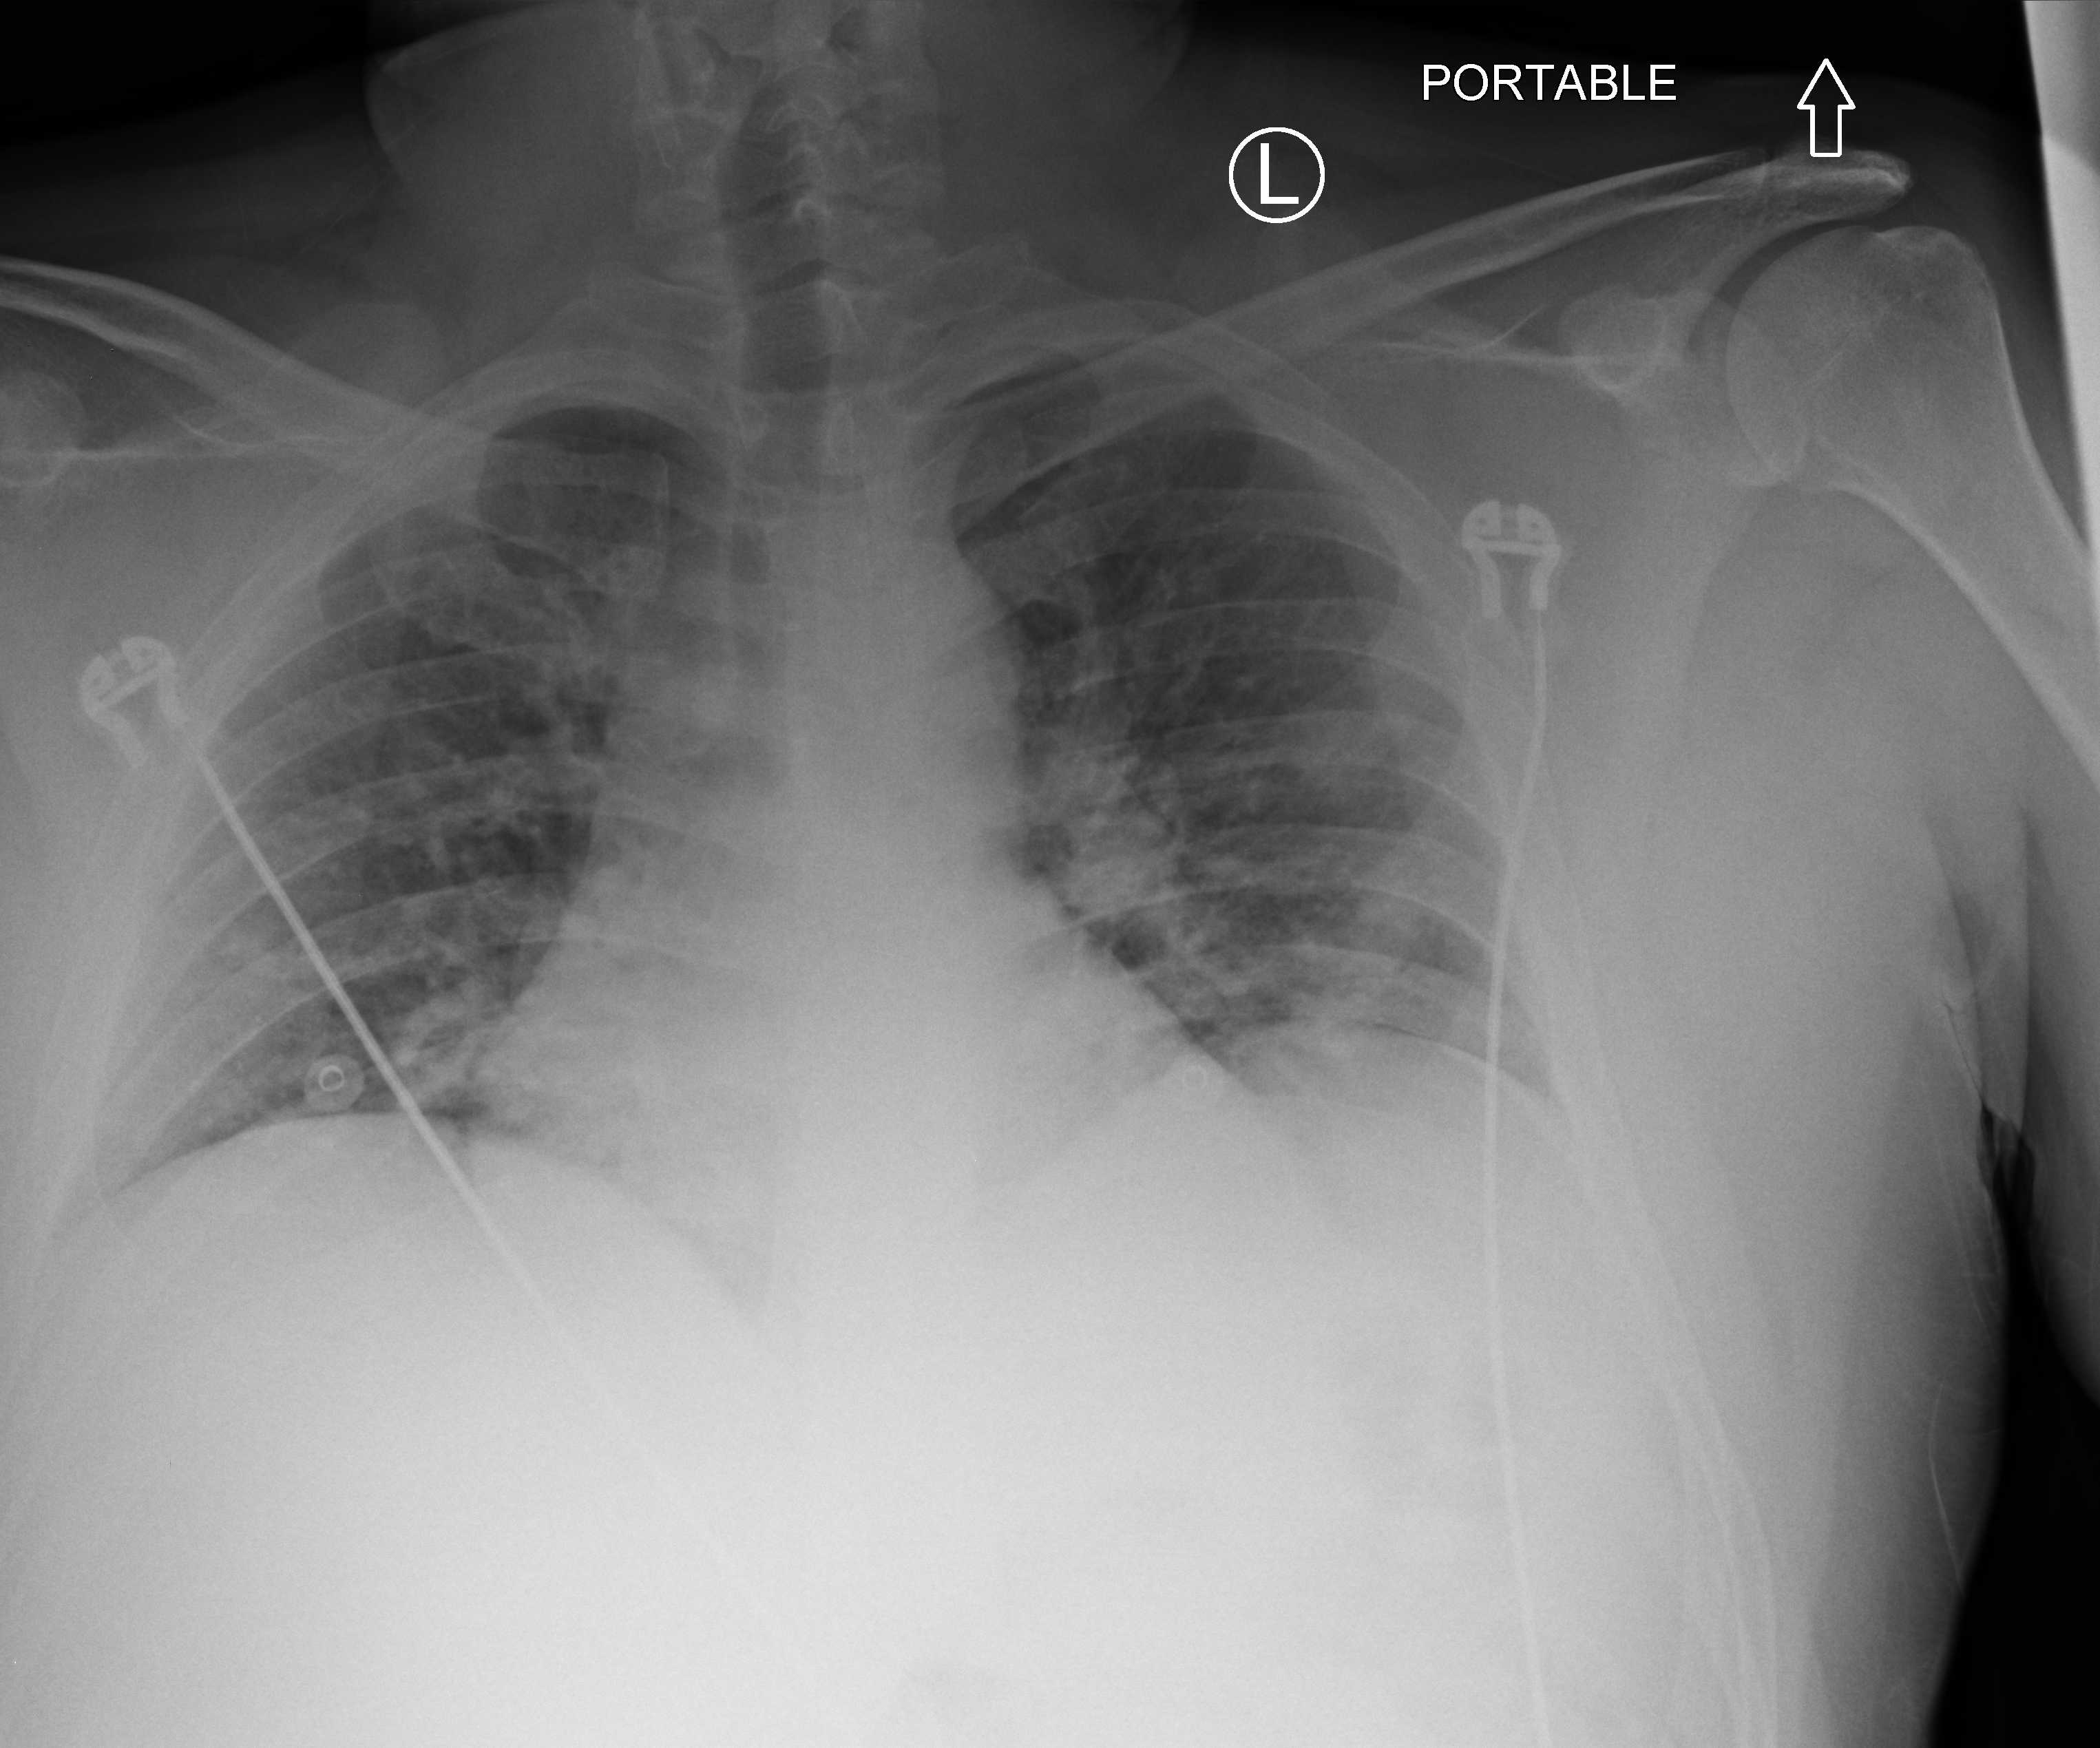
Chest X-ray (portable); anteroposterior (AP) projection. Male patient hospitalised with COVID-19, age 18–59 years.
Hospital-stay facts (about this admission, not read from this image; timing relative to this image not recorded): admitted to intensive care during this hospital stay: no; mechanically ventilated during this hospital stay: no; length of hospital stay: 1 day.